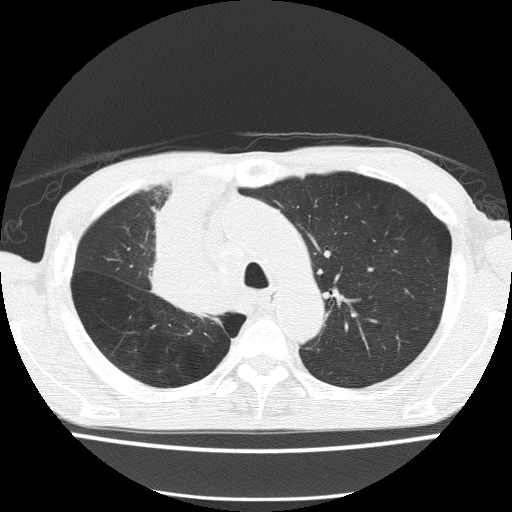
Low-dose screening chest CT, axial slice; baseline screening round; lung window (W 1500 / L -600 HU); 2 mm slice thickness; lung (sharp) reconstruction kernel (FC51). Male, age 59 years at enrolment. Former smoker at enrolment.
Expert reader's lesion annotation, box from (x=134, y=233) to (x=237, y=325) px. The screening reader recorded 5 non-calcified nodules or masses ≥4 mm on this exam (left upper lobe, left upper lobe, left upper lobe, right middle lobe, right lower lobe); which of them this box marks is not recorded. Official screen result: positive, change unspecified: nodule(s) >= 4 mm or enlarging nodule(s), mass(es), or other non-specific abnormalities suspicious for lung cancer. Later outcome: lung cancer diagnosed 72 days after this screen — squamous cell carcinoma, NOS, right upper lobe, moderately differentiated (G2), stage IV (AJCC 6th edition).